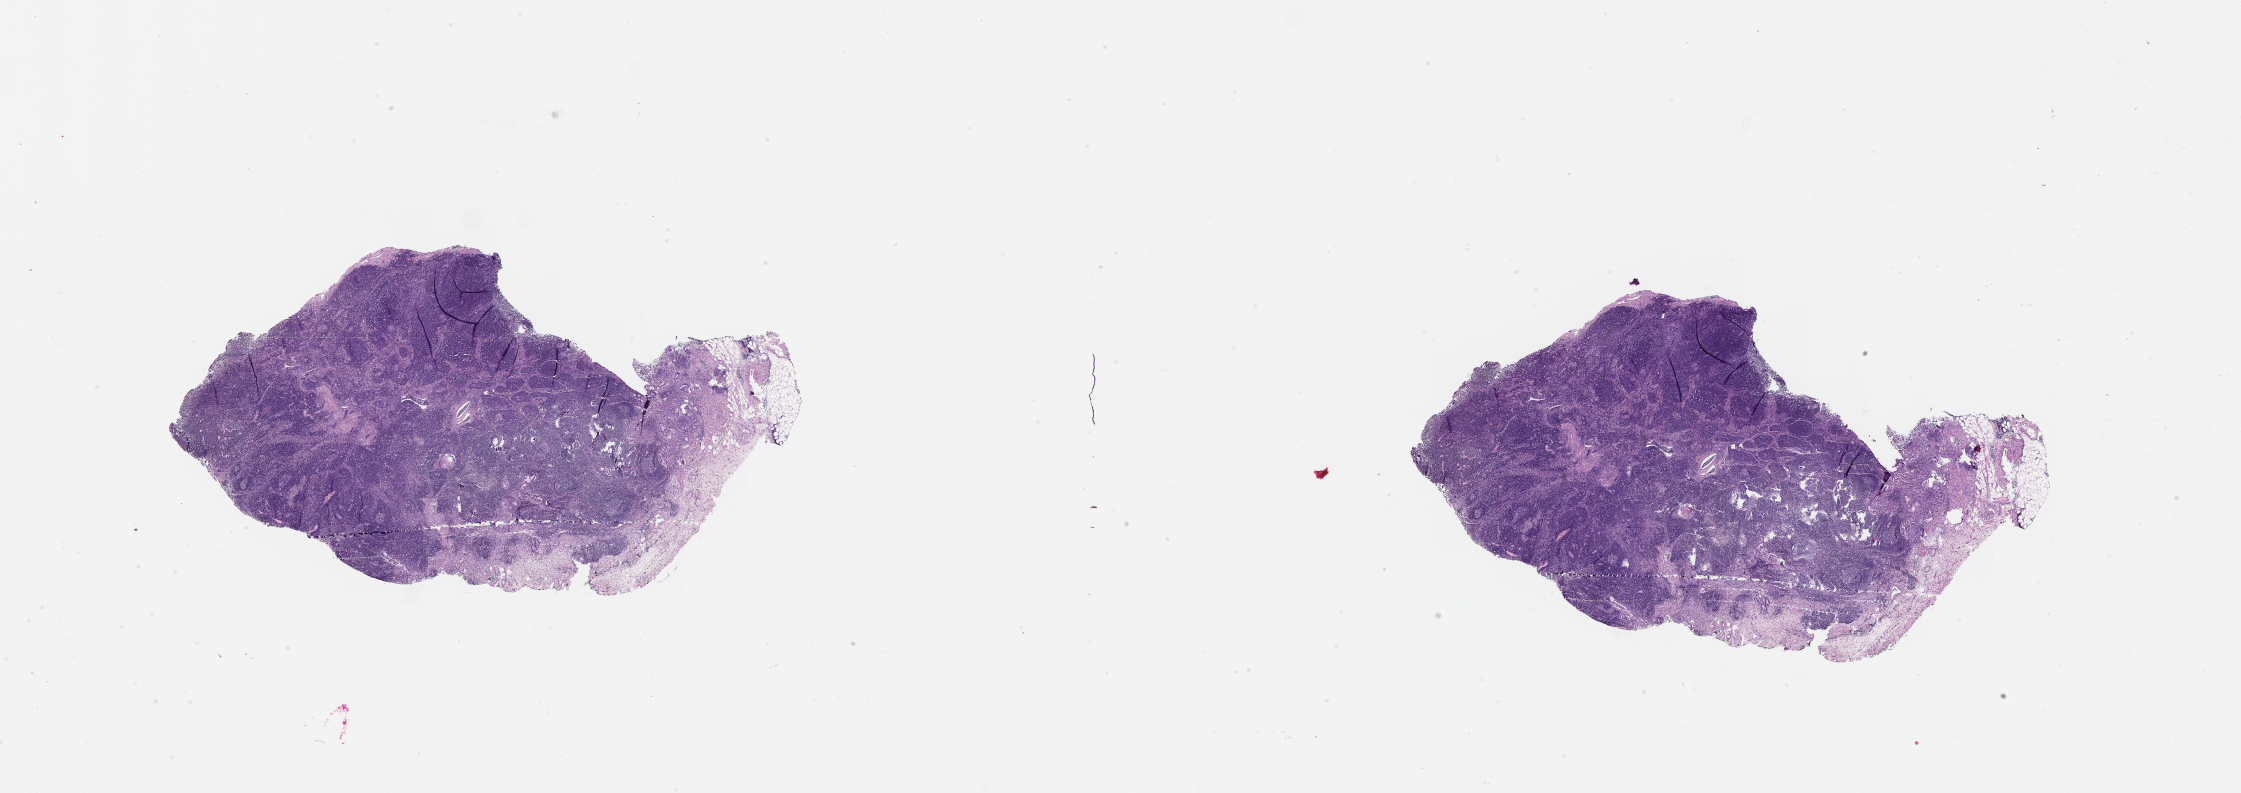
Hematoxylin and eosin (H&E) stained whole-slide image, shown as a low-resolution overview of the whole scanned area (about 36.1 x 12.8 mm, slide scanned at 20x). Normal (non-tumour) tissue sample, pancreas. Patient: male, age 69 years.
• this section: normal (non-tumour) tissue from the same patient
• patient diagnosis: Infiltrating duct carcinoma, NOS